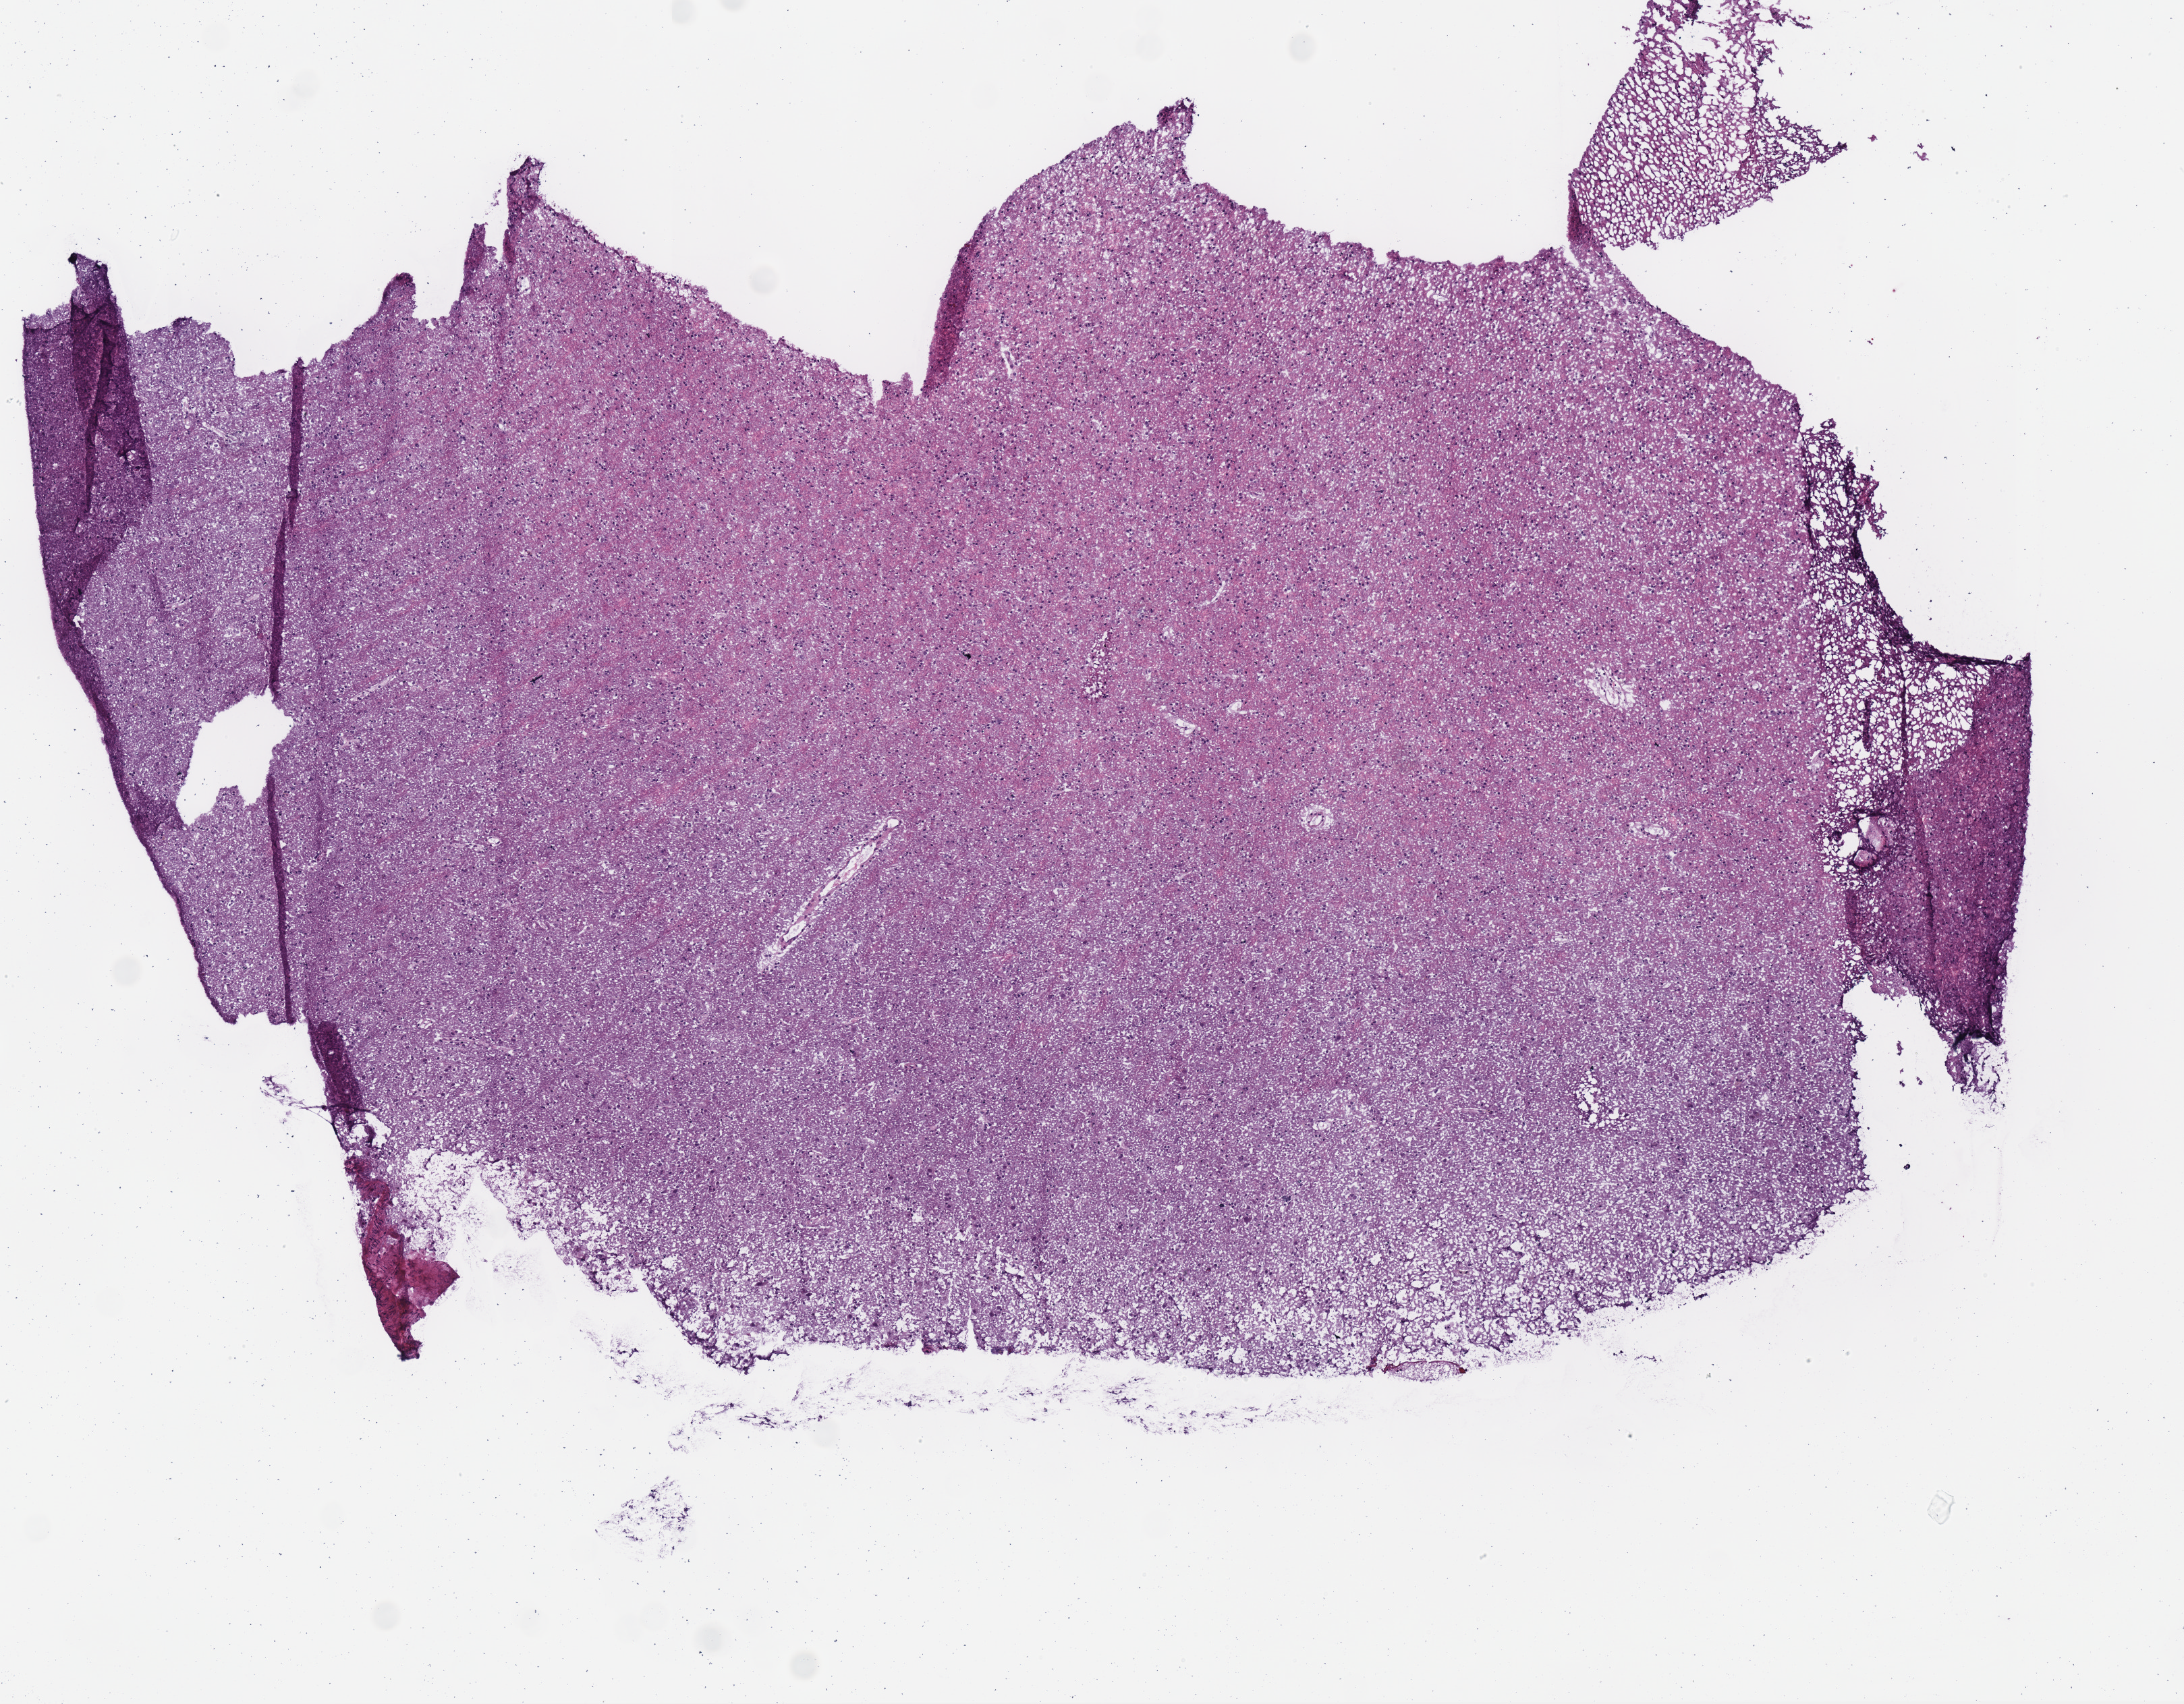
Digitized H&E tissue section (whole slide) — a low-resolution overview of the entire scanned area, about 6.4 x 5.0 mm, frozen section from the bottom of the tissue portion, sample: primary tumour, brain. Patient: female, age at initial diagnosis 49 years. Histologic grade: G2 (moderately differentiated). Pathologist review of this section (percent, as recorded): tumour cells 100%, tumour nuclei 65%, normal cells 0%, stromal cells 0%, necrosis 0%.
- laterality: left
- histologic diagnosis: Oligodendroglioma, NOS